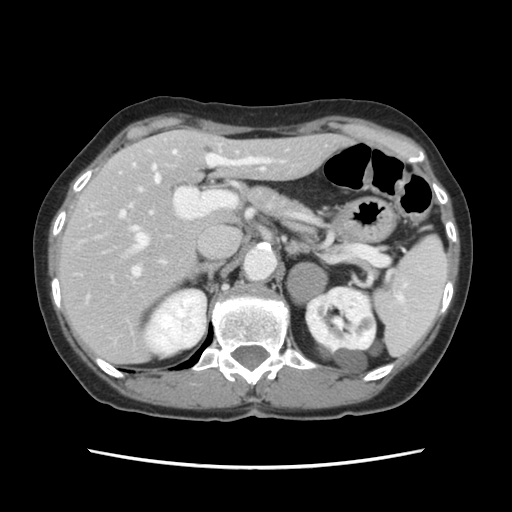
Contrast-enhanced abdominal CT, one axial slice; slice 80 of 120 in the series (ordered by position); 120 kVp; intravenous contrast given; soft-tissue window (W 400 / L 40 HU); 2.5 mm slice thickness; 512 × 512 image matrix. Female patient, age 70 years. From the clinical record (not read from this slice): diagnosis: colorectal cancer liver metastases, imaged before liver resection; multiple liver metastases: no; largest metastasis: 2.5 cm.
Annotated regions visible in this slice (expert manual segmentation):
- hepatic veins: bounding box [x1, y1, x2, y2] px = [133, 150, 177, 250]
- liver: [60, 131, 342, 363]
- planned liver remnant (the part of the liver to remain after resection): [97, 130, 344, 286]
- portal vein (with intrahepatic branches): [119, 154, 283, 277]